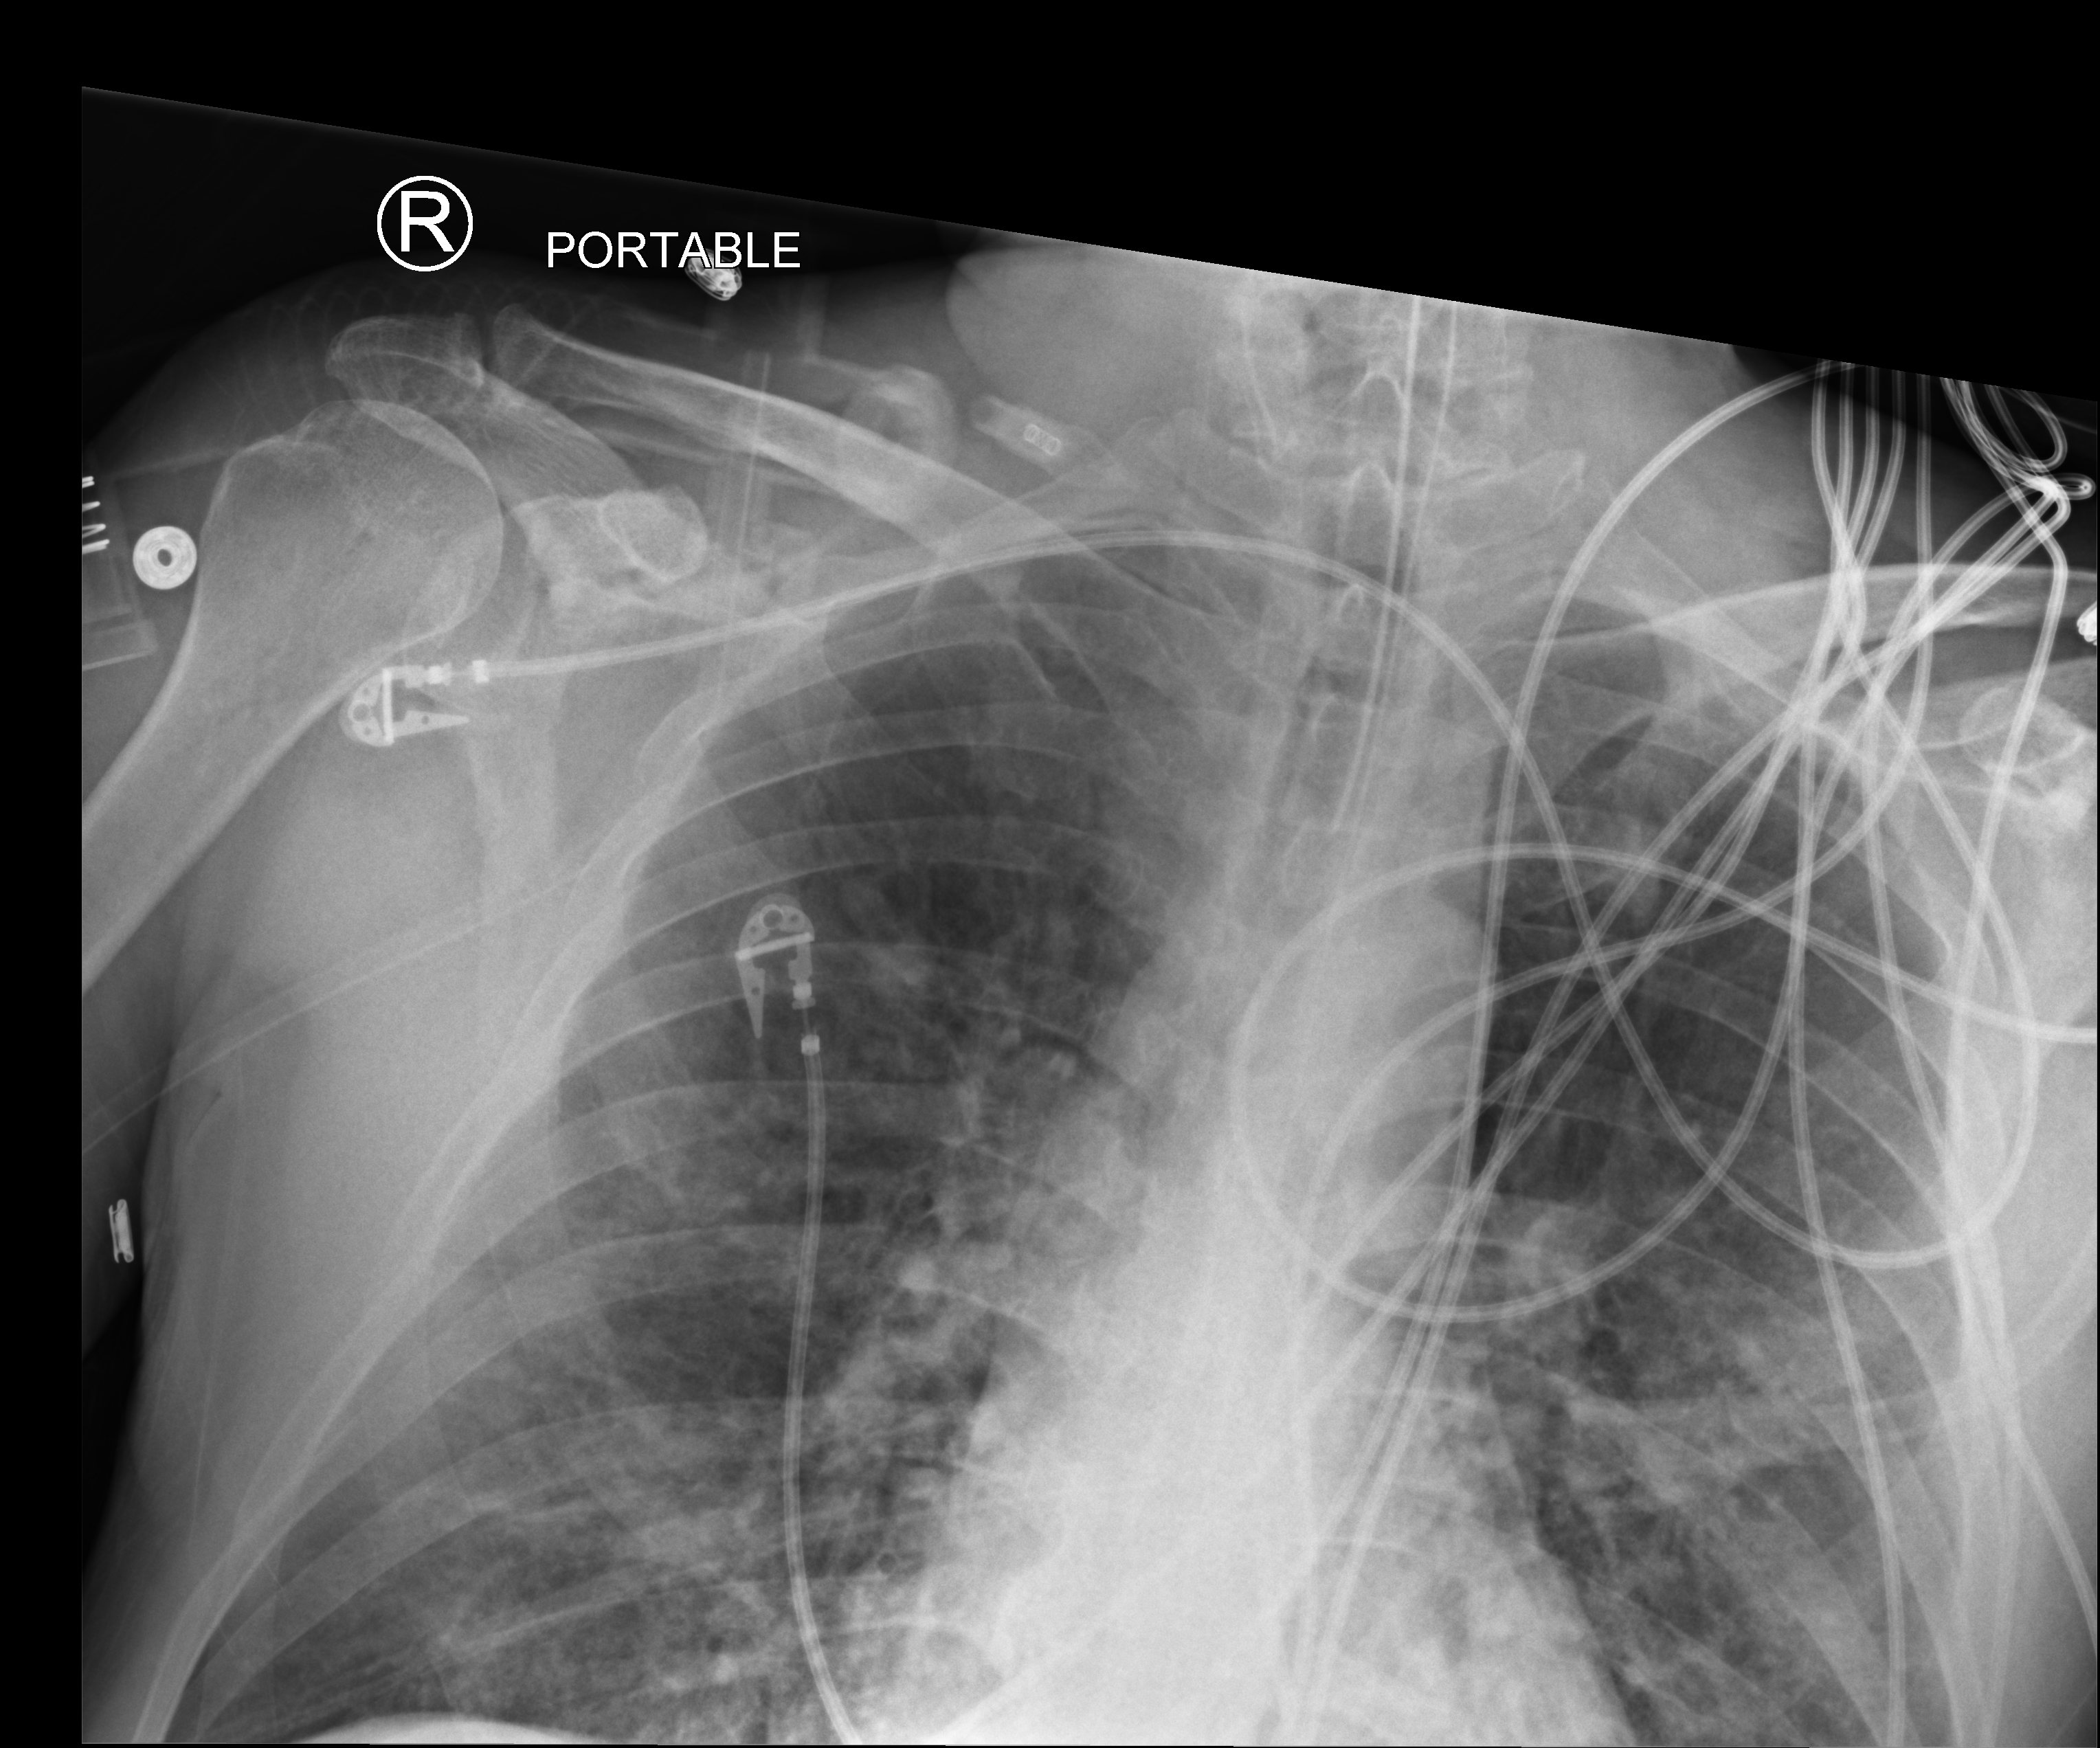
Chest X-ray (portable); anteroposterior (AP) projection. Male patient hospitalised with COVID-19, age 18–59 years.
Hospital-stay facts (about this admission, not read from this image; timing relative to this image not recorded): mechanically ventilated during this hospital stay: yes.